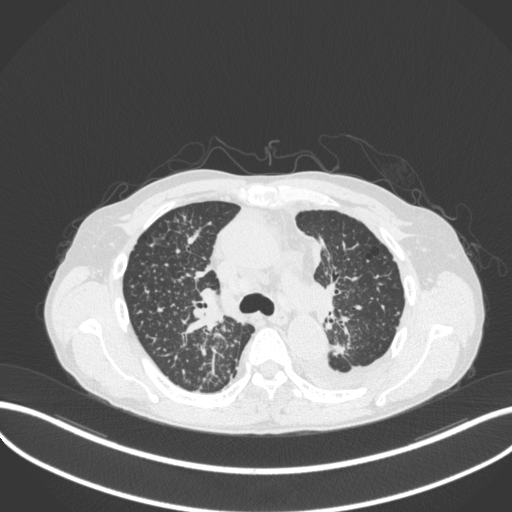
Chest CT, one axial slice; position 243 of 319 along the scan axis; reconstruction kernel B31f; 120 kVp; lung window (W 1500 / L -600 HU); 512 × 512 image matrix, field of view 400 × 400 mm. Patient: male, 58 years. Case-level facts recorded for this patient, not image findings: clinical TNM (as recorded): T1c N3 M1.
Structures marked on this image (rectangle marked by the reading radiologist):
- lung tumour (recorded histology: adenocarcinoma): box from (x=327, y=338) to (x=351, y=363) px